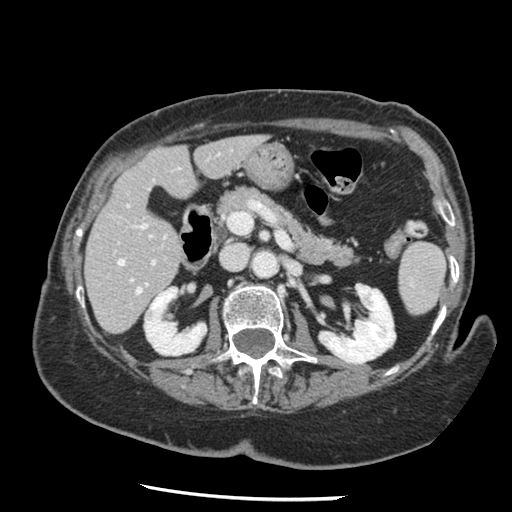
Contrast-enhanced abdominal CT, one axial slice. Slice 63 of 148 in the series (ordered by position). 120 kVp. Intravenous contrast given. Soft-tissue window (W 400 / L 40 HU). 2.5 mm slice thickness. 512 × 512 image matrix, field of view 330 × 330 mm. Female patient, age 85 years. From the clinical record (not read from this slice): diagnosis: colorectal cancer liver metastases, imaged before liver resection; multiple liver metastases: no; largest metastasis: 0.9 cm.
Outlined on this slice (manually delineated by an expert):
- hepatic veins: box from (x=118, y=259) to (x=141, y=293) px
- liver: (x=86, y=136)–(x=262, y=333)
- planned liver remnant (the part of the liver to remain after resection): (x=86, y=136)–(x=262, y=325)
- portal vein (with intrahepatic branches): (x=127, y=204)–(x=156, y=283)